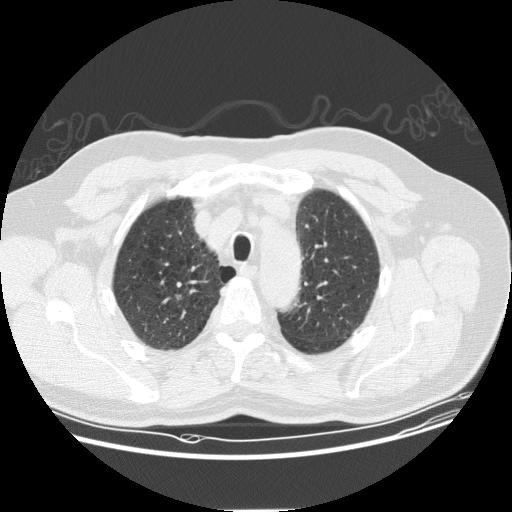
Low-dose screening chest CT, axial slice, first (baseline) screen, lung window (W 1500 / L -600 HU), slice 32 of 157 in the series. Male participant, aged 61 years at enrolment. Former smoker at enrolment.
Expert reader's lesion annotation, bounding box [x1, y1, x2, y2] px = [155, 281, 199, 319]. Screening reader's record for this exam: no non-calcified nodule ≥4 mm recorded. Official screen result: negative screen, minor abnormalities not suspicious for lung cancer. Lung cancer was diagnosed 832 days after this screen: squamous cell carcinoma, NOS, right upper lobe, moderately differentiated (G2), stage IA (AJCC 6th edition), 10 mm at pathology.